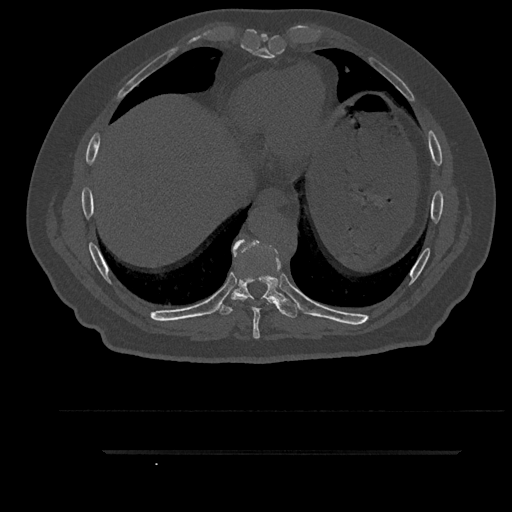
CT including the spine, one axial slice; position 445 of 797 along the scan axis; bone window (W 1800 / L 400 HU); 512 × 512 image matrix, field of view 432 × 432 mm. Male patient, age 63 years. From the clinical record (not read from this slice): primary cancer: renal; vertebrae with lytic lesions (as recorded): T8.
Annotated regions visible in this slice (semi-automatic segmentation, software-assisted and operator-edited):
- T8 vertebra: bounding box (x1, y1, x2, y2) in pixels: (232, 239, 279, 339)
- T9 vertebra: (214, 244, 298, 318)